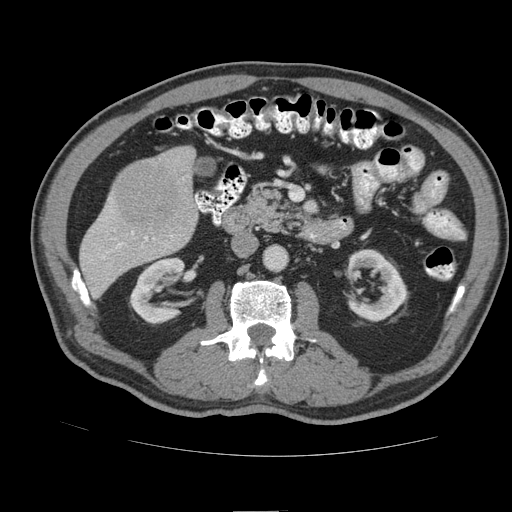
Contrast-enhanced abdominal CT (liver protocol), one axial slice. Slice 31 of 105 in the series (ordered by position). 140 kVp. Soft-tissue window (W 400 / L 40 HU). 2.5 mm slice thickness. 512 × 512 image matrix, field of view 380 × 380 mm. From the clinical record (not read from this slice): diagnosis: hepatocellular carcinoma (patient treated with transarterial chemoembolisation; whether this scan precedes or follows treatment is not stated here); TNM stage (as recorded): Stage-IIIB; Child-Pugh class: A.
Annotated regions visible in this slice (semi-automatic segmentation, software-assisted and operator-edited):
- liver parenchyma outside the tumour (the mass and vessels are separate outlines, so this box may not span the whole liver): bounding box <80,146,196,296> (left, top, right, bottom; pixels)
- mass: <118,162,181,230>
- liver vessels: <118,232,148,246>